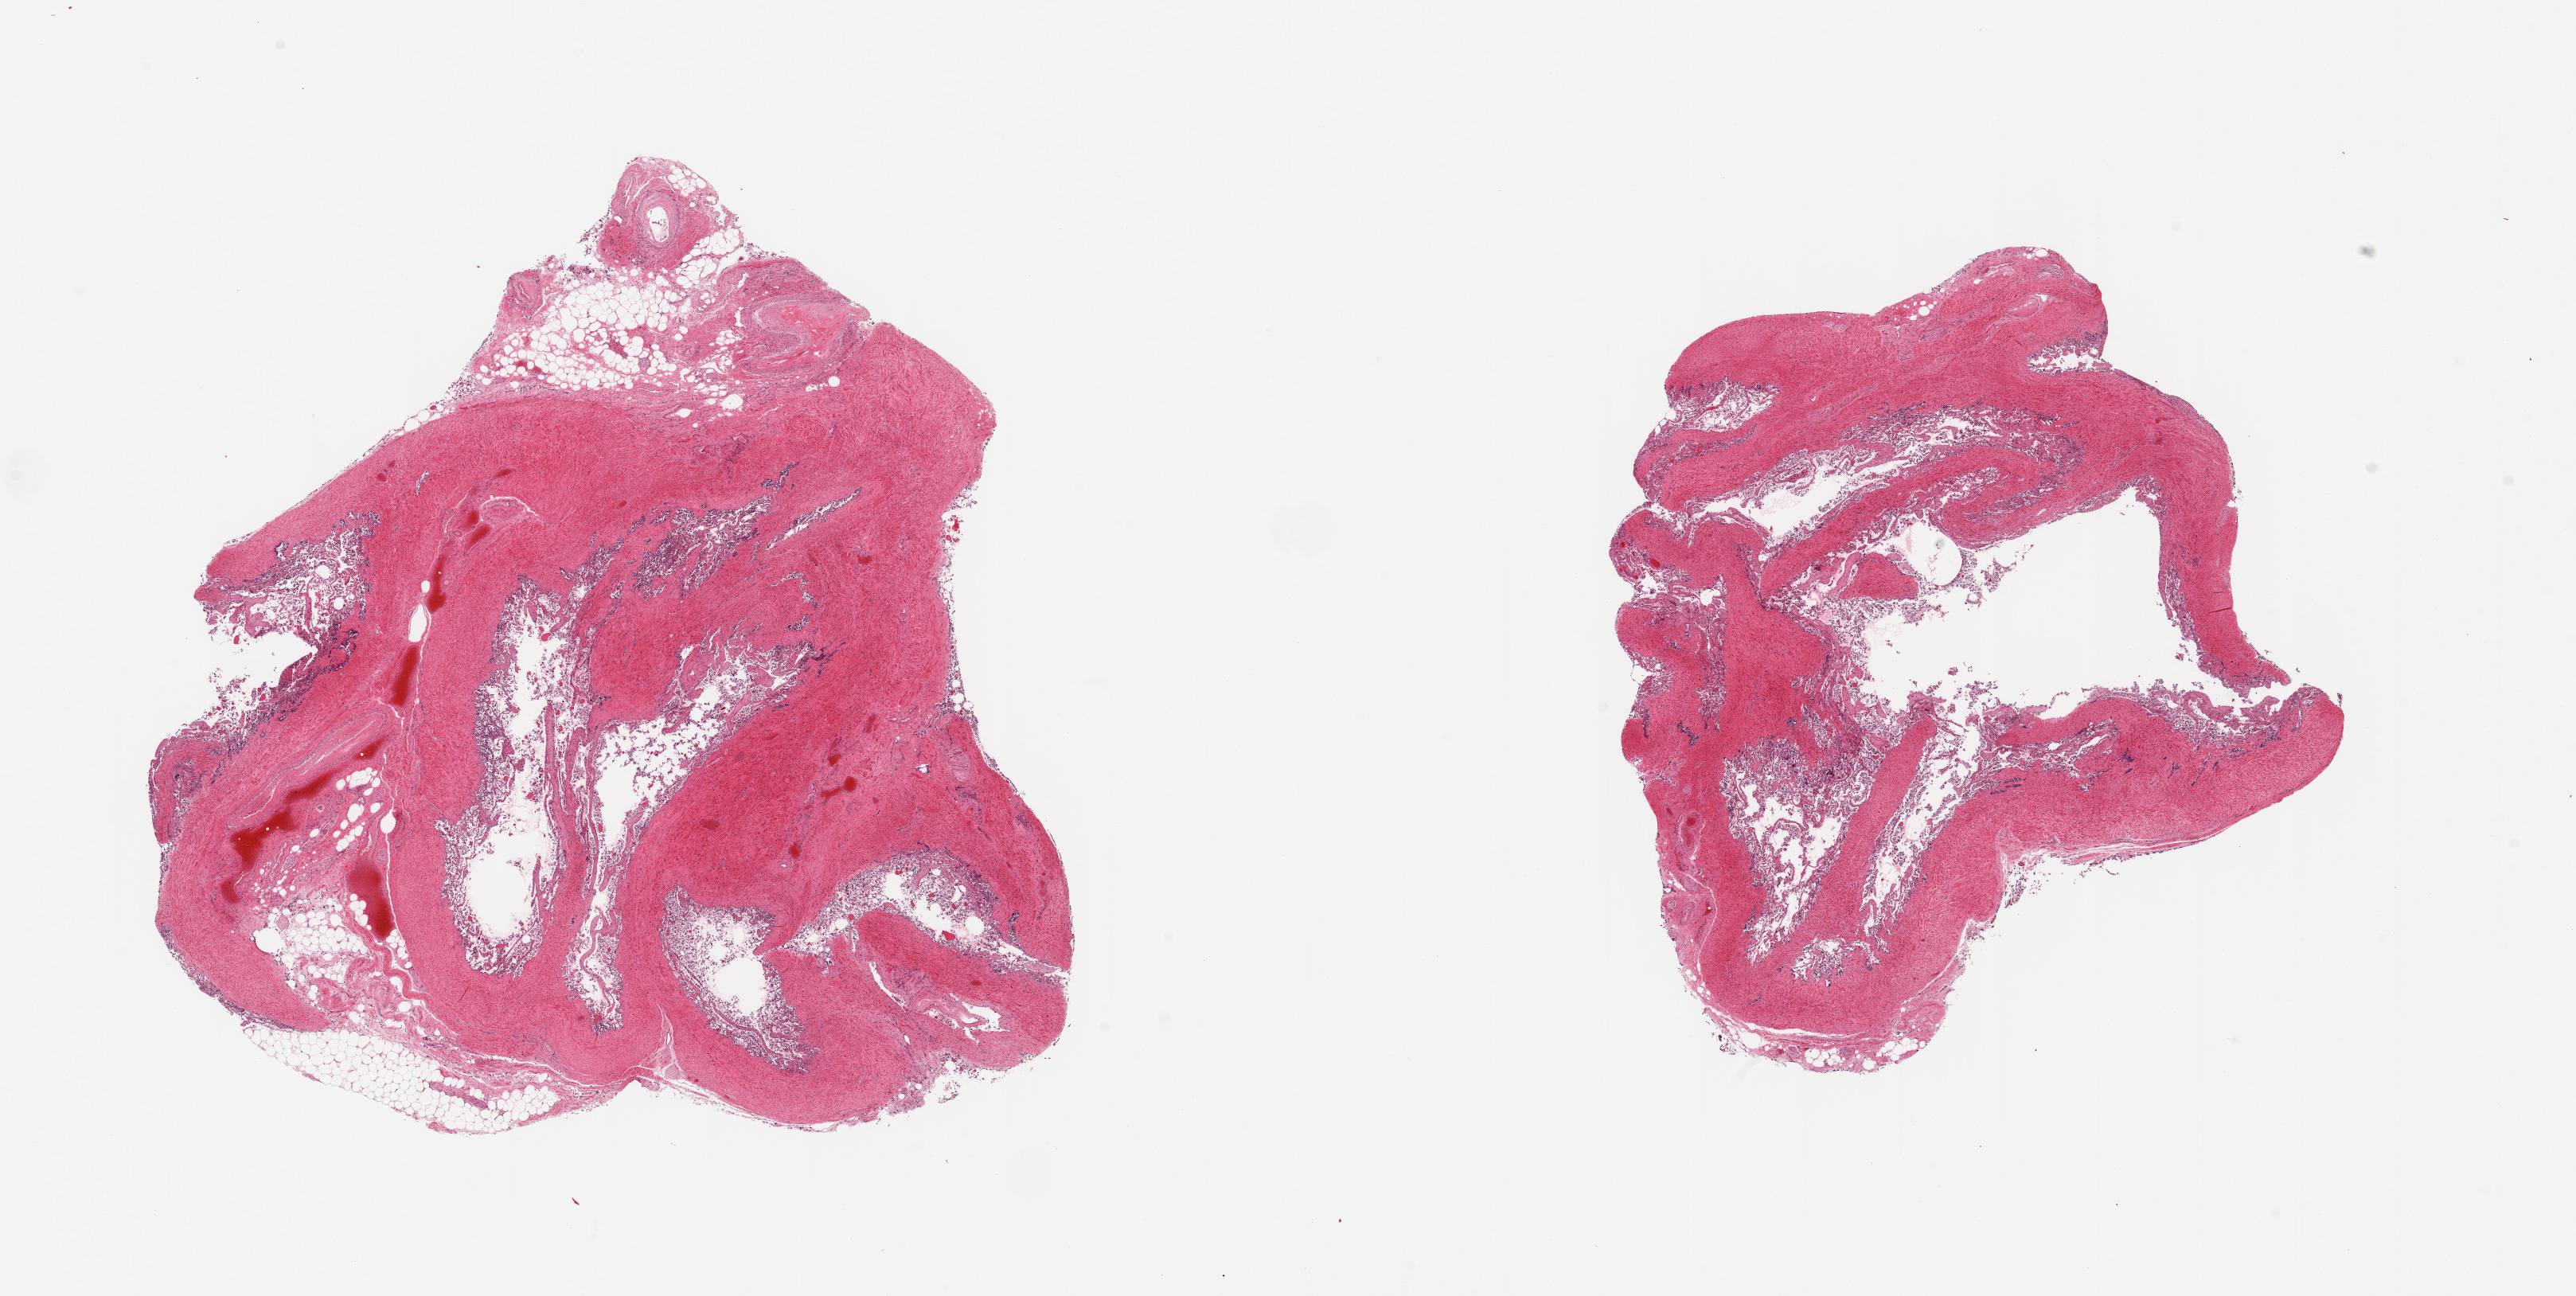
Whole-slide image, haematoxylin and eosin stain, brightfield — shown as a low-resolution overview of the whole scanned area (about 25.6 x 12.9 mm, acquisition: 20x scan). PAXgene-fixed, paraffin-embedded tissue. Section of prostate (target tissue). Donor tissue sample. Donor: male.
• pathologist's review note for this sample: 2 pieces; seminal vesicle, not prostate